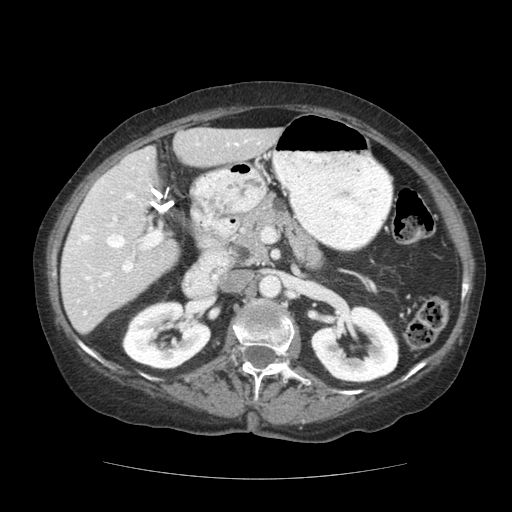
Contrast-enhanced abdominal CT (liver protocol), one axial slice. Position 64 of 111 along the scan axis. 140 kVp. Soft-tissue window (W 400 / L 40 HU). 2.5 mm slice thickness. 512 × 512 image matrix, field of view 360 × 360 mm. From the clinical record (not read from this slice): diagnosis: hepatocellular carcinoma (patient treated with transarterial chemoembolisation; whether this scan precedes or follows treatment is not stated here); TNM stage (as recorded): Stage-I; Child-Pugh class: A; tumour nodularity: uninodular.
Structures marked on this image (semi-automatic segmentation, software-assisted and operator-edited):
- liver parenchyma outside the tumour (the mass and vessels are separate outlines, so this box may not span the whole liver): box from (x=60, y=128) to (x=280, y=332) px
- liver vessels: (x=66, y=139)–(x=261, y=315)